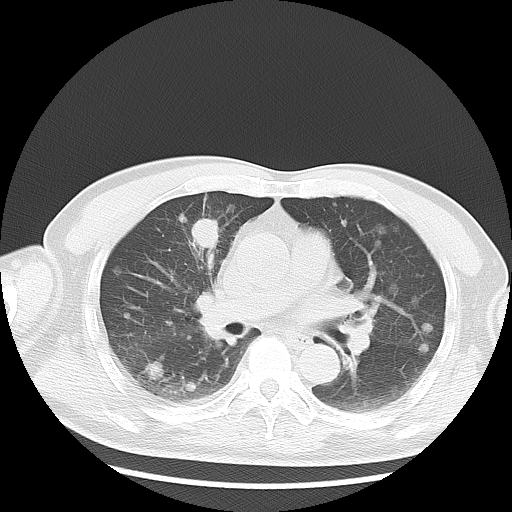
Chest CT, one axial slice; position 12 of 35 along the scan axis; 120 kVp; lung window (W 1500 / L -600 HU); 5 mm slice thickness; 512 × 512 image matrix, field of view 369 × 369 mm. Male patient, age 57 years. From the clinical record (not read from this slice): clinical TNM (as recorded): T2 N3 M1a.
Annotated regions visible in this slice (rectangle marked by the reading radiologist):
- lung tumour (recorded histology: adenocarcinoma): box from (x=187, y=215) to (x=221, y=250) px